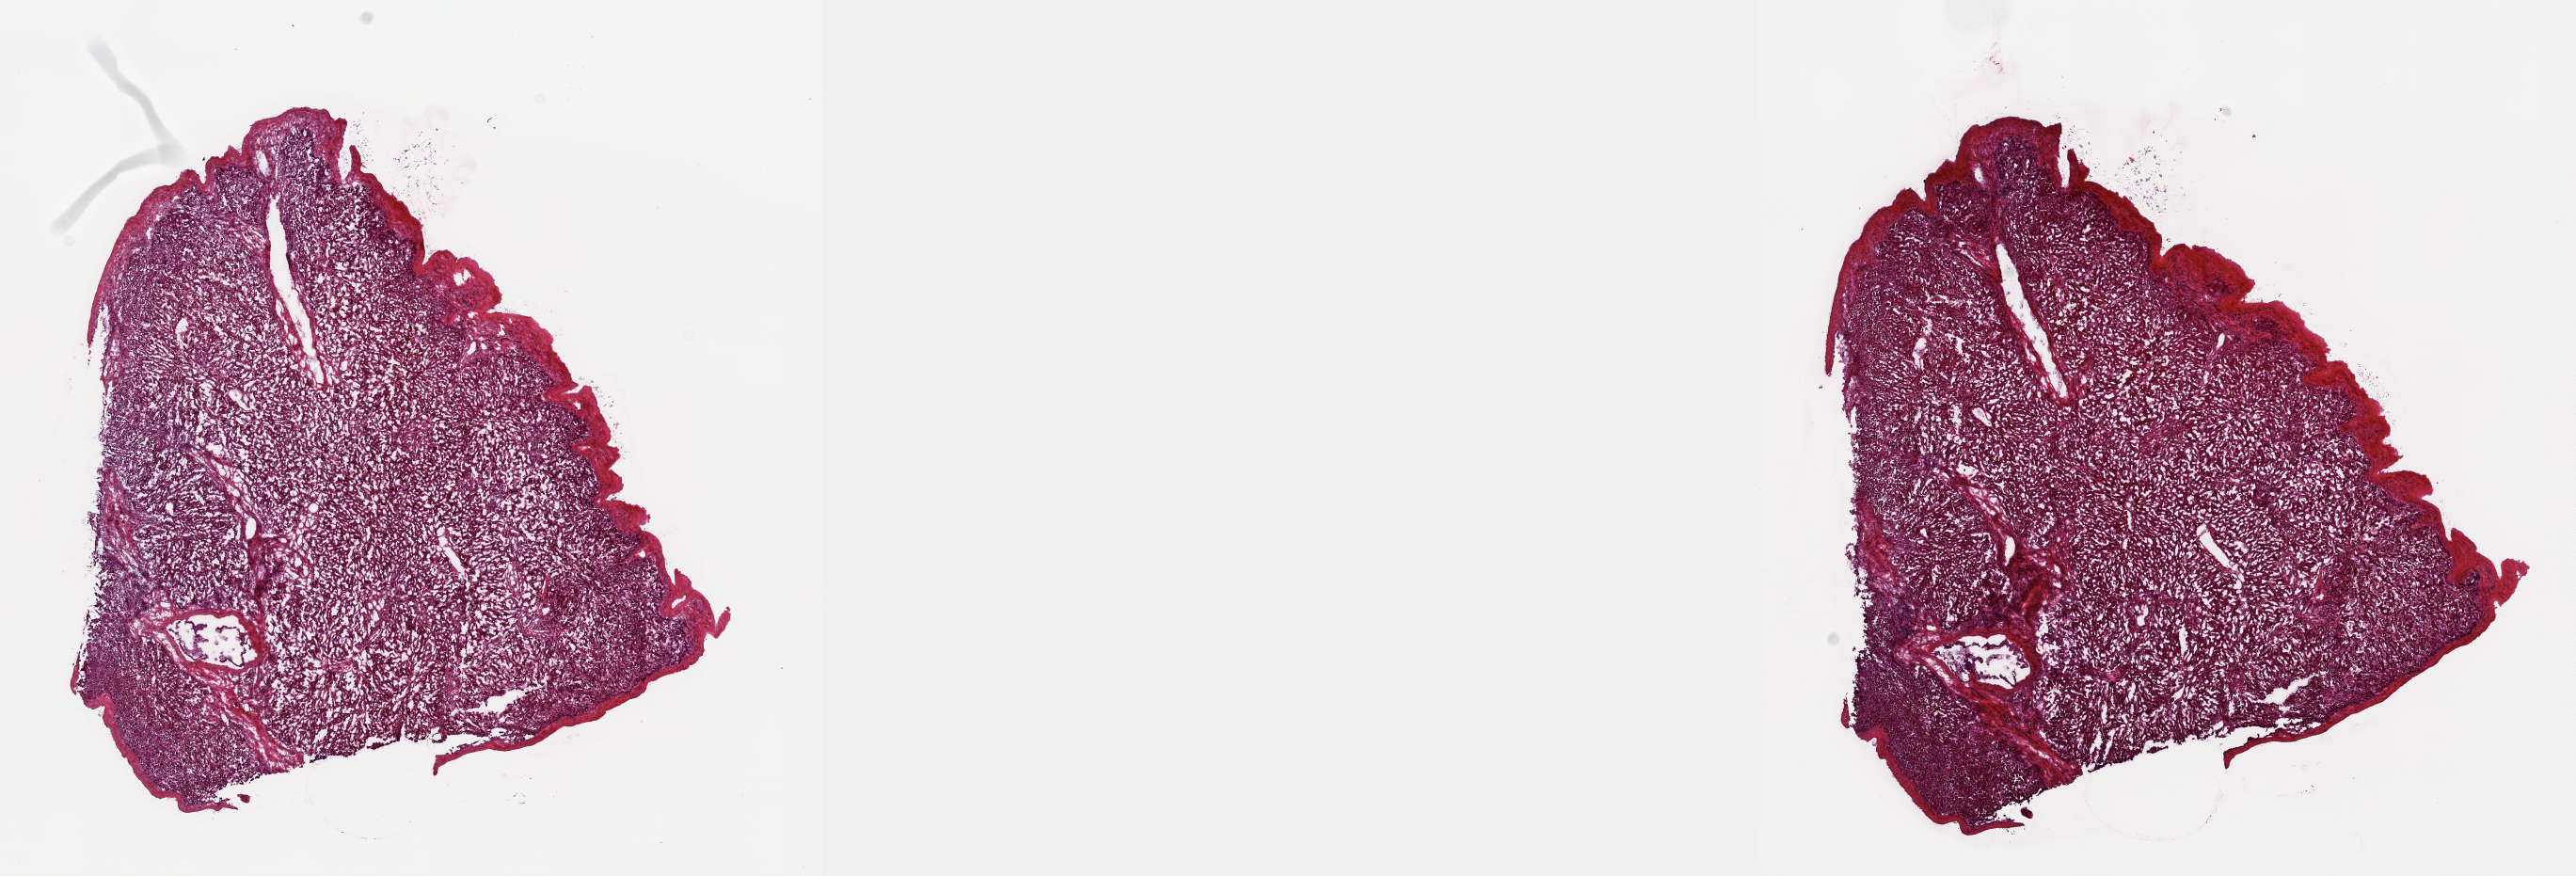
Whole-slide histology image, H&E — low-resolution overview of the scanned area, about 22.1 x 7.5 mm, frozen section from the top of the tissue portion, bile duct, solid tissue normal (non-tumour tissue) sample. Patient: male, age at initial diagnosis 74 years. Slide review estimates, as recorded: tumour cells 0%, tumour nuclei 0%.
This section: solid tissue normal (non-tumour) sample from the same patient. Patient diagnosis: Cholangiocarcinoma (intrahepatic bile duct).